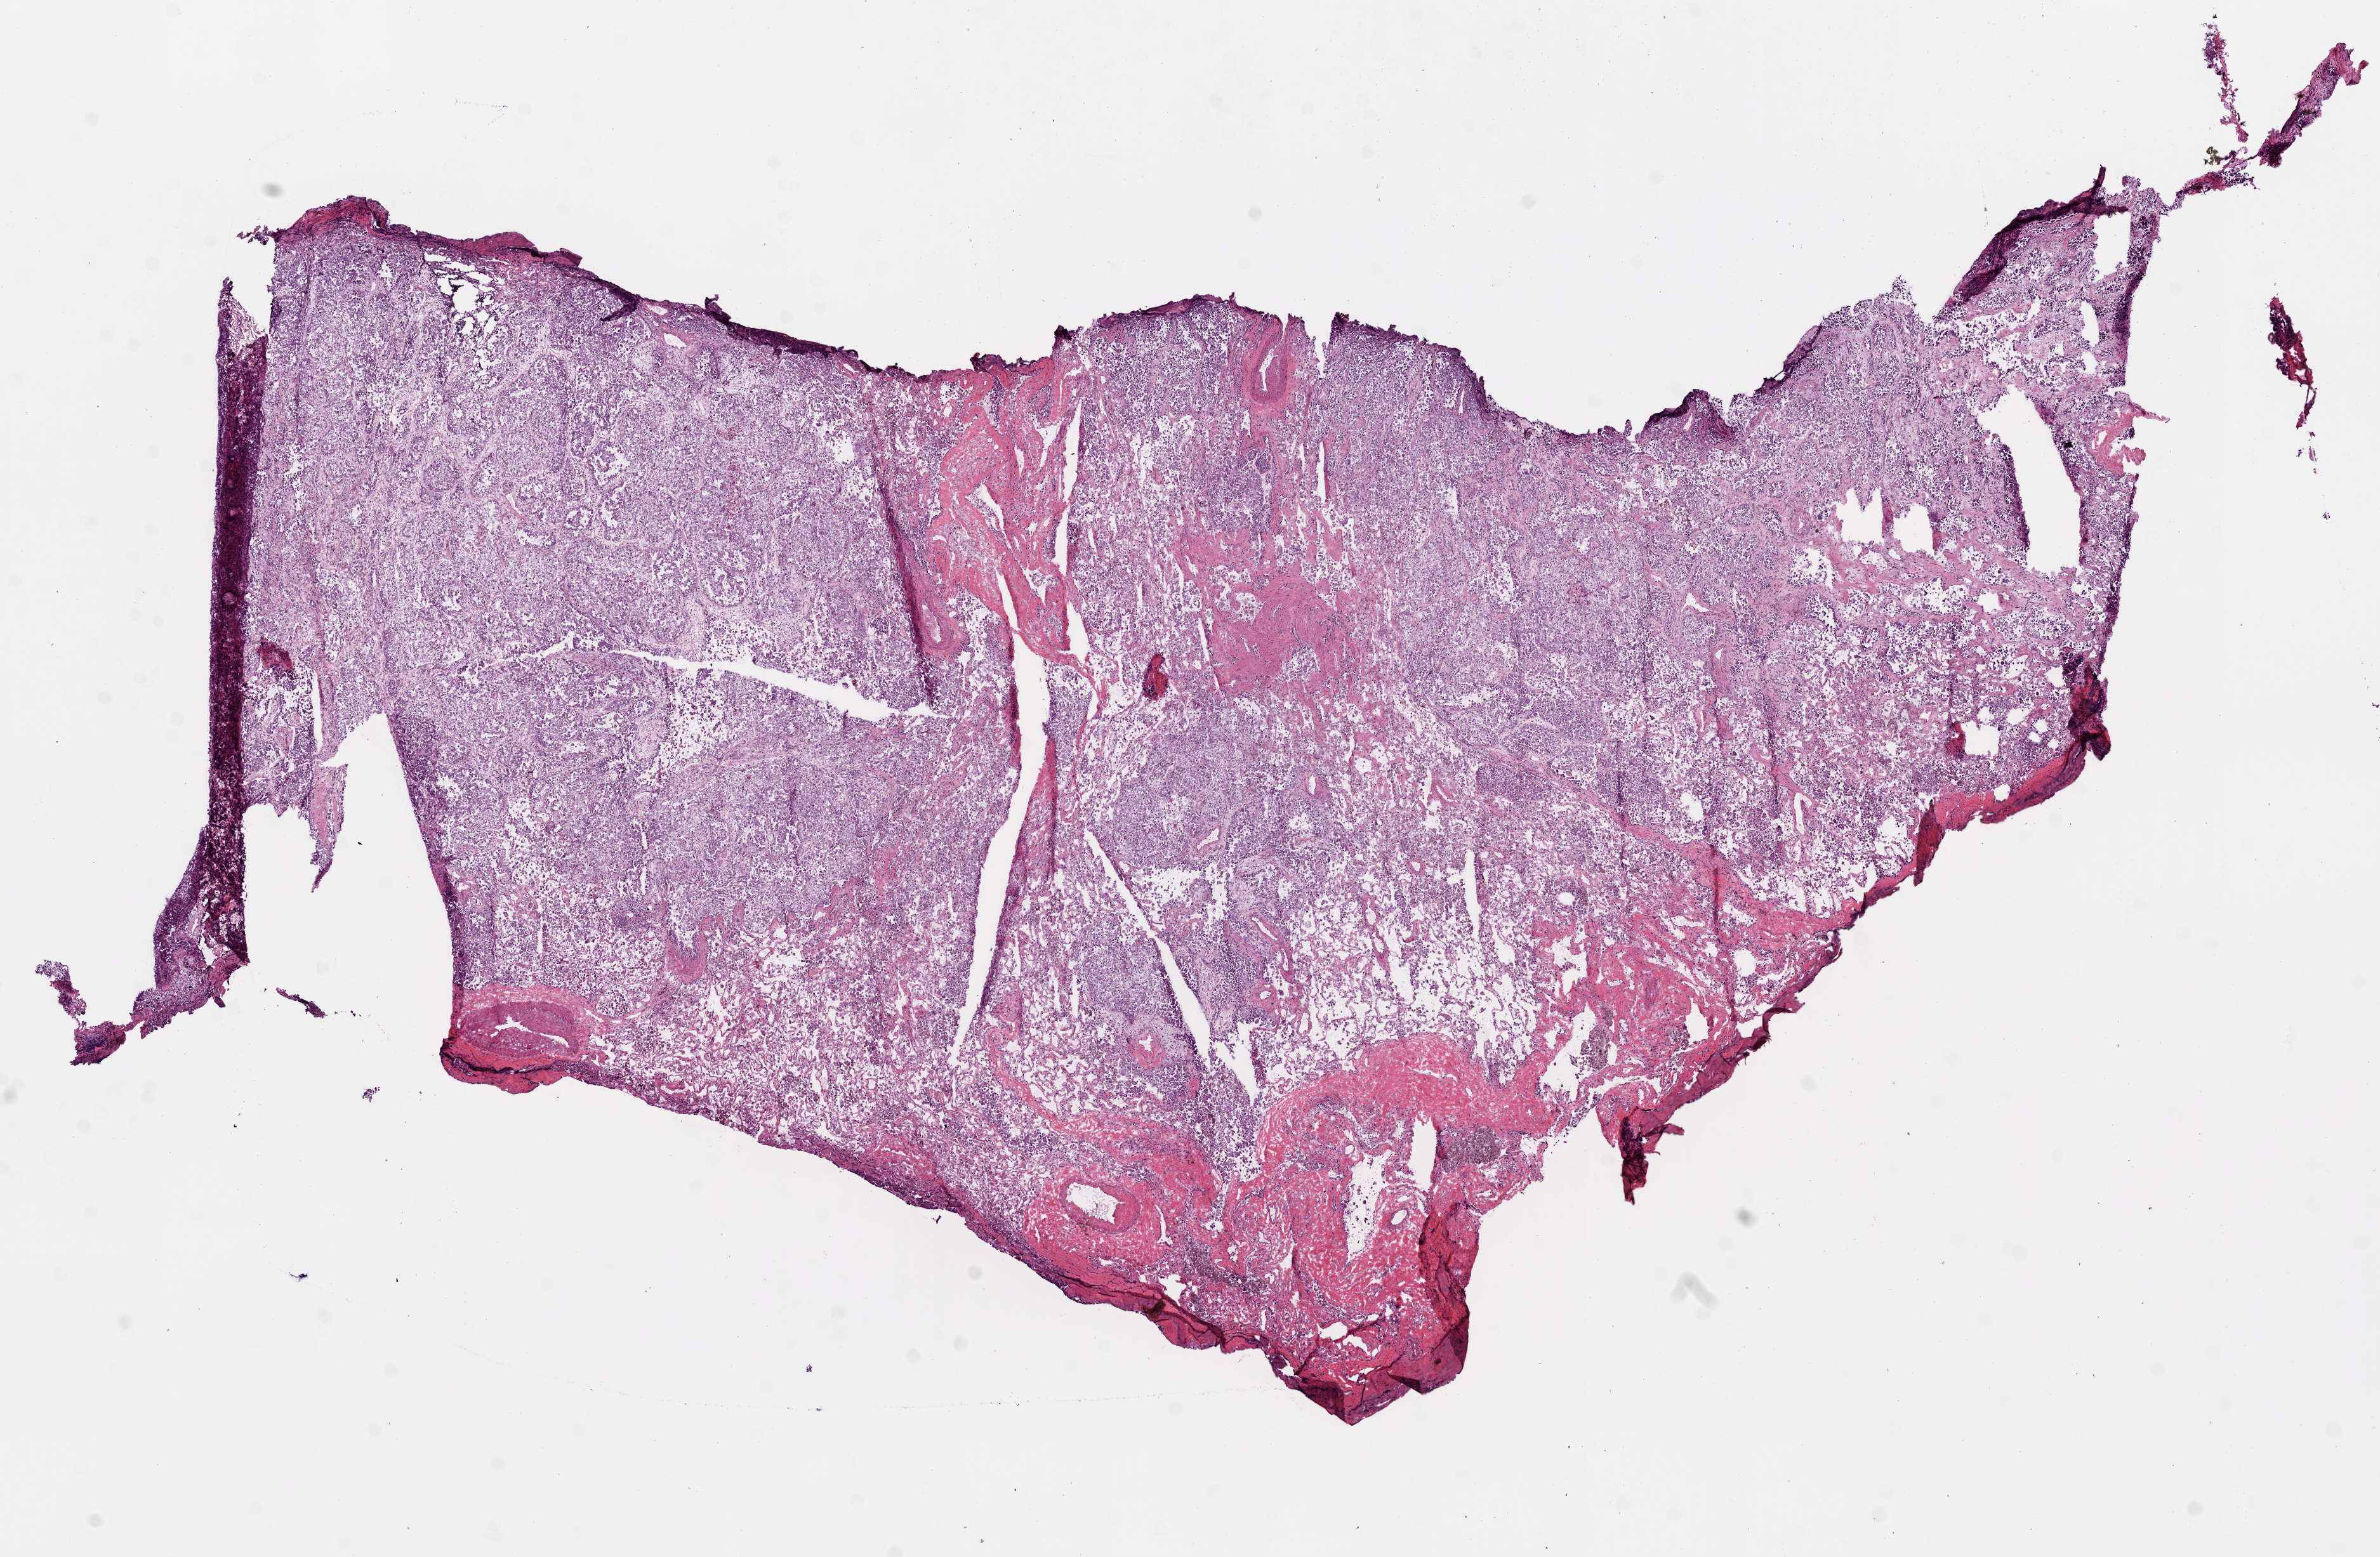
Digitized H&E tissue section (whole slide) — shown as a low-resolution overview of the whole scanned area (about 15.0 x 9.8 mm); frozen section; primary tumour sample from the lung. Patient: male, age at initial diagnosis 45 years. Composition of this section per pathologist review: tumour cells 50%, tumour nuclei 80%, normal cells 0%, stromal cells 20%, necrosis 30%.
Pathologic diagnosis: Adenocarcinoma, NOS (upper lobe, lung). AJCC pathologic stage: IIA (7th edition). TNM: T2a N1 M0.